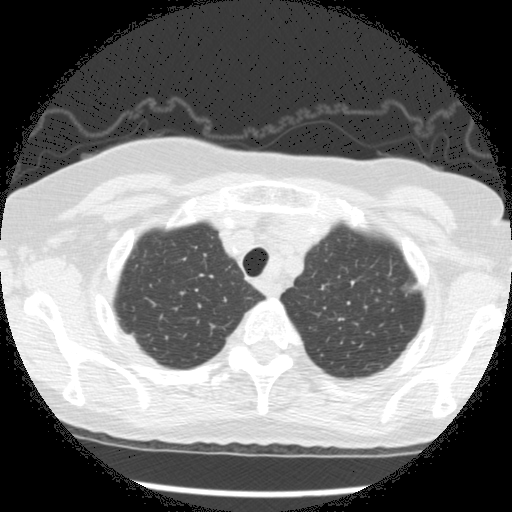
Low-dose screening chest CT, one axial slice; slice 235 of 266 in the series (ordered by position); 120 kVp; lung window (W 1500 / L -600 HU); 512 × 512 image matrix, field of view 320 × 320 mm.
Outlined on this slice (manually delineated by an expert):
- lesion 1 (tumor, upper lobe of left lung): bounding box <411,285,419,291> (left, top, right, bottom; pixels)